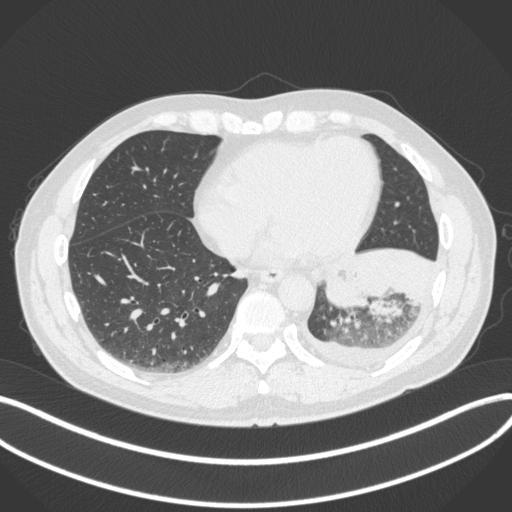
Chest CT, one axial slice; slice 115 of 350 in the series (ordered by position); reconstruction kernel B31f; 120 kVp; lung window (W 1500 / L -600 HU); 512 × 512 image matrix, field of view 400 × 400 mm. Male patient, age 58 years. From the clinical record (not read from this slice): clinical TNM (as recorded): T3 N1 M1b; histopathological grade: G3.
Structures marked on this image (rectangle marked by the reading radiologist):
- lung tumour (recorded histology: small cell carcinoma): bounding box [x1, y1, x2, y2] px = [323, 266, 371, 314]